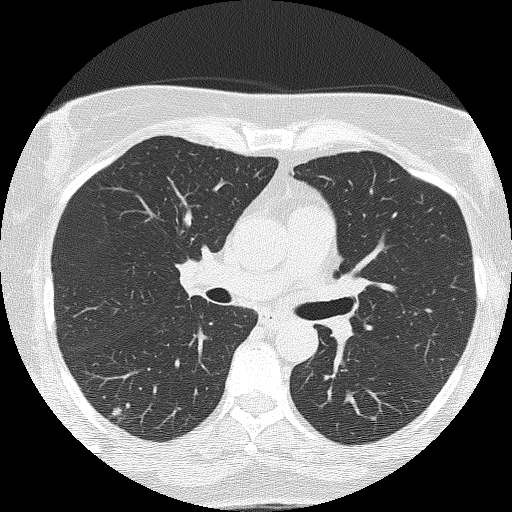
Low-dose screening chest CT, one axial slice; slice 82 of 143 in the series (ordered by position); 120 kVp; lung window (W 1500 / L -600 HU); 2 mm slice thickness; 512 × 512 image matrix, field of view 301 × 301 mm.
Annotated regions visible in this slice (outlined manually by an expert reader):
- lesion 1 (tumor, lower lobe of right lung): bounding box (x1, y1, x2, y2) in pixels: (113, 408, 121, 416)